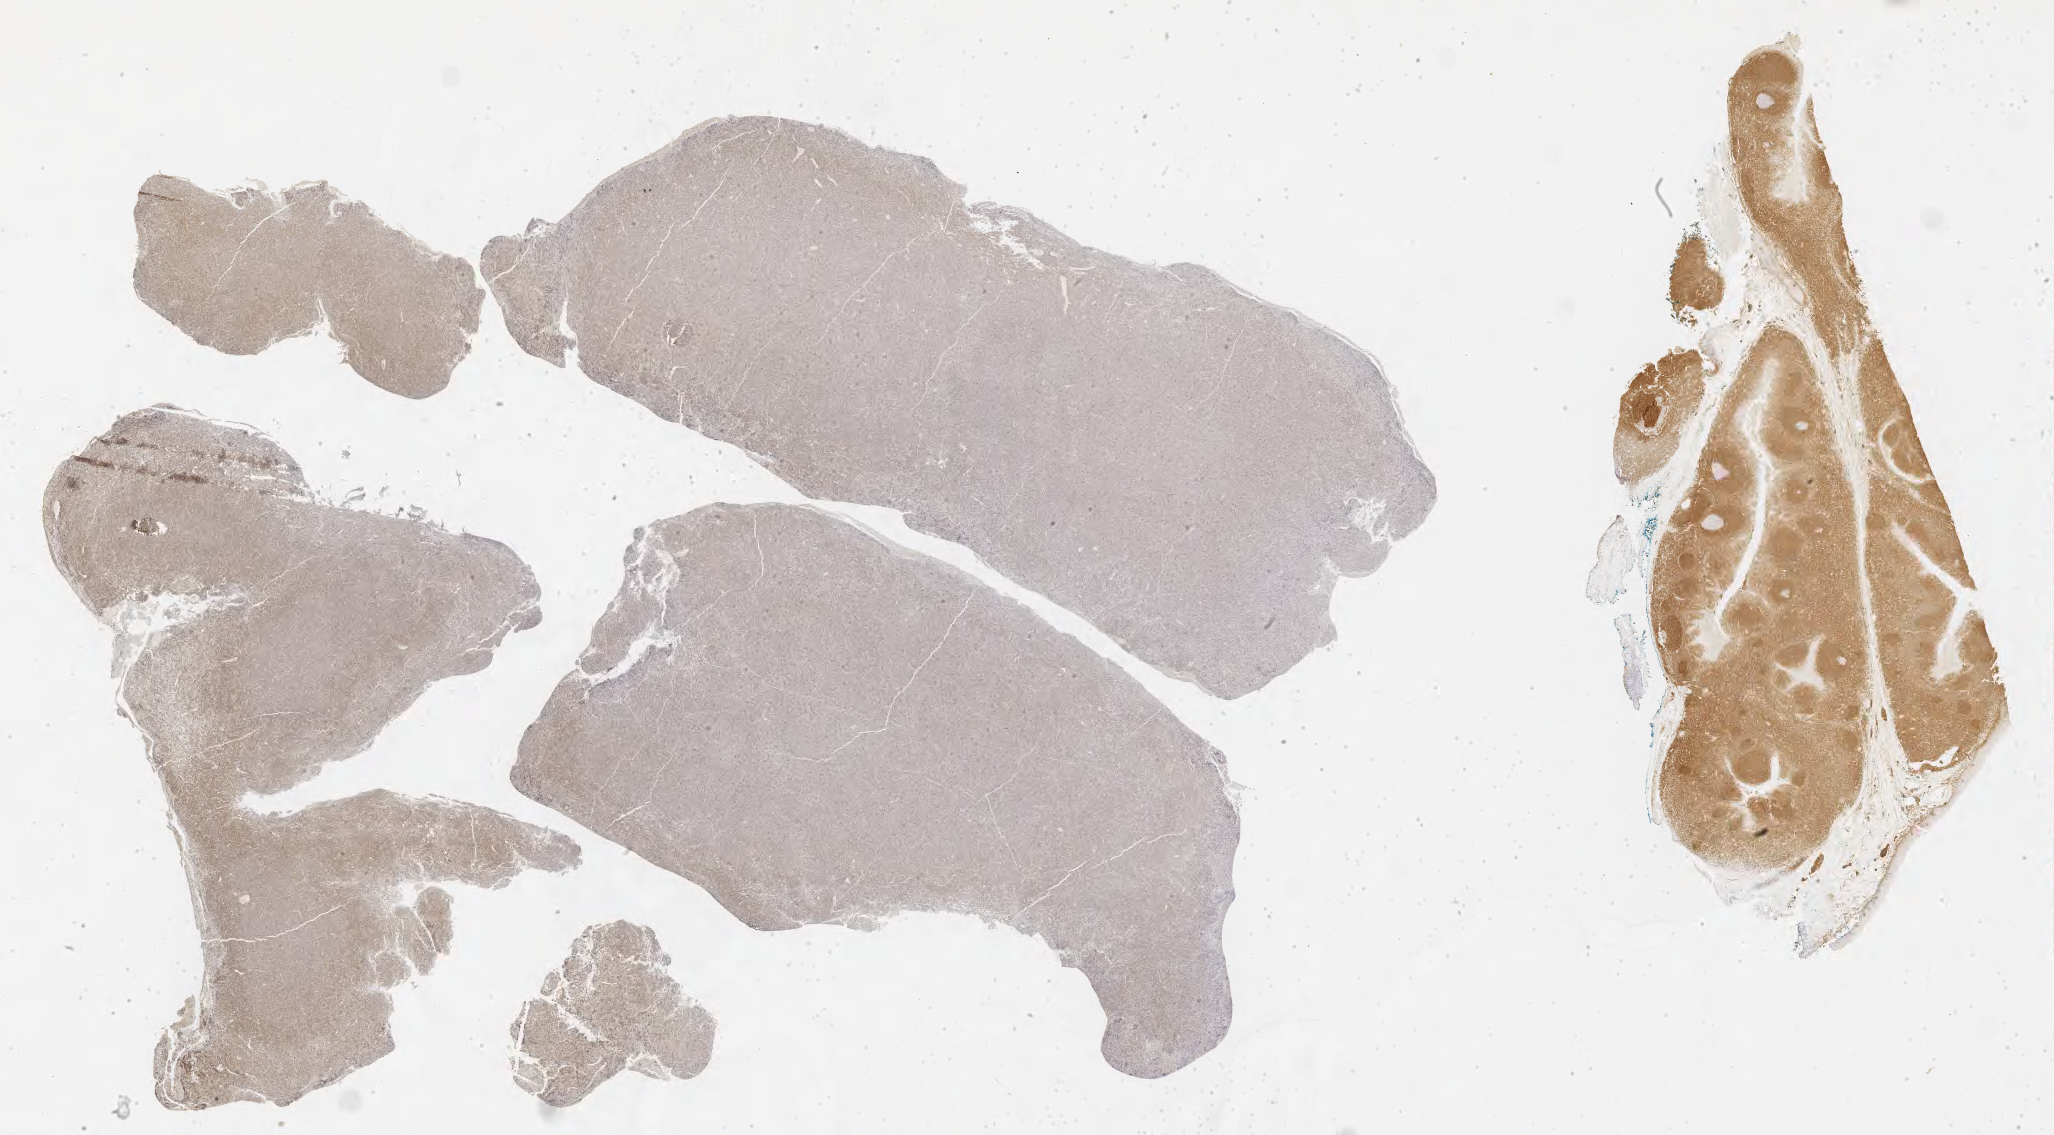
Immunohistochemistry (IHC) whole-slide image stained for BCL2, whole scanned area (about 33.2 x 18.4 mm) shown as a low-resolution overview. Tumor tissue. Site: peritoneum. Patient: female, age at initial diagnosis 7 years.
Diagnosis: Burkitt lymphoma, NOS.